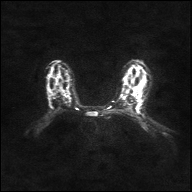
Breast MRI, one axial slice; position 21 of 36 along the scan axis; diffusion-weighted series; image 2 of 4 stored at this slice position (different b-values; order by instance number); 1.5 T; 4 mm slice thickness; 192 × 192 image matrix, field of view 360 × 360 mm. Female patient.
Annotated regions visible in this slice (manually delineated by an expert):
- tumour on diffusion-weighted imaging: bounding box <49,101,52,105> (left, top, right, bottom; pixels)